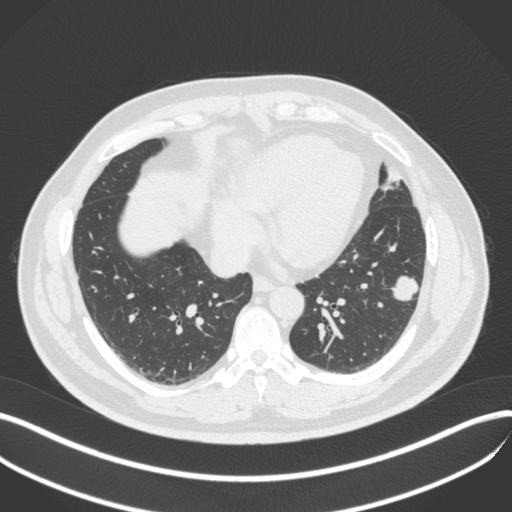
Chest CT, one axial slice. Slice 148 of 420 in the series (ordered by position). Reconstruction kernel B31f. Lung window (W 1500 / L -600 HU). 1 mm slice thickness. 512 × 512 image matrix, field of view 400 × 400 mm. Male patient, age 39 years. From the clinical record (not read from this slice): clinical TNM (as recorded): T2a N0 M0; histopathological grade: G2-3.
Outlined on this slice (bounding box drawn by a radiologist):
- lung tumour (recorded histology: adenocarcinoma): bounding box [x1, y1, x2, y2] px = [387, 271, 424, 307]